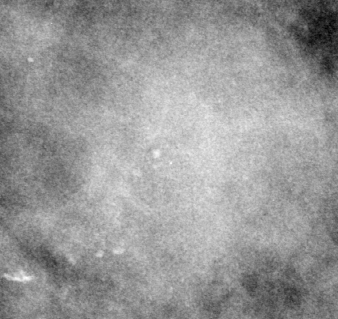
Cropped region of a digitized screen-film mammogram centred on a radiologist-marked abnormality; left breast; MLO view; BI-RADS breast density category 4 (scale 1–4).
- Mass, shape oval, margins circumscribed; BI-RADS assessment category 3; subtlety rating 3 on a 1 (subtle) to 5 (obvious) scale; pathology result (as recorded, not read from the image): benign.